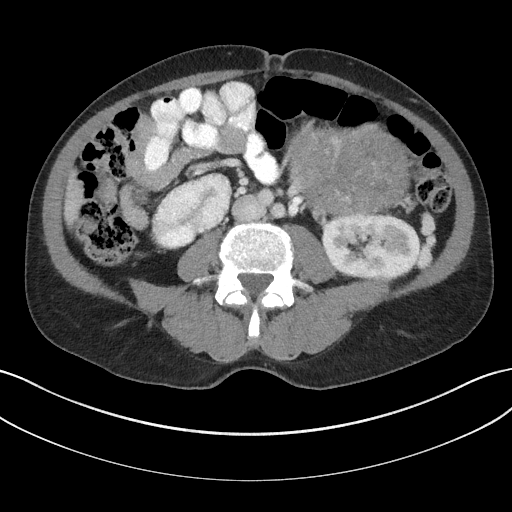
Contrast-enhanced abdominal CT, one axial slice; position 76 of 147 along the scan axis; reconstruction kernel I31f/3; 100 kVp; soft-tissue window (W 400 / L 40 HU); 512 × 512 image matrix. Patient: male, 58 years. Case-level facts recorded for this patient, not image findings: diagnosis: adrenocortical carcinoma; tumour side: left adrenal; tumour size at pathology: 22 cm; Ki-67 index: 26 %.
Annotated regions visible in this slice (semi-automatic segmentation, software-assisted and operator-edited):
- mass: bounding box (x1, y1, x2, y2) in pixels: (289, 125, 407, 215)